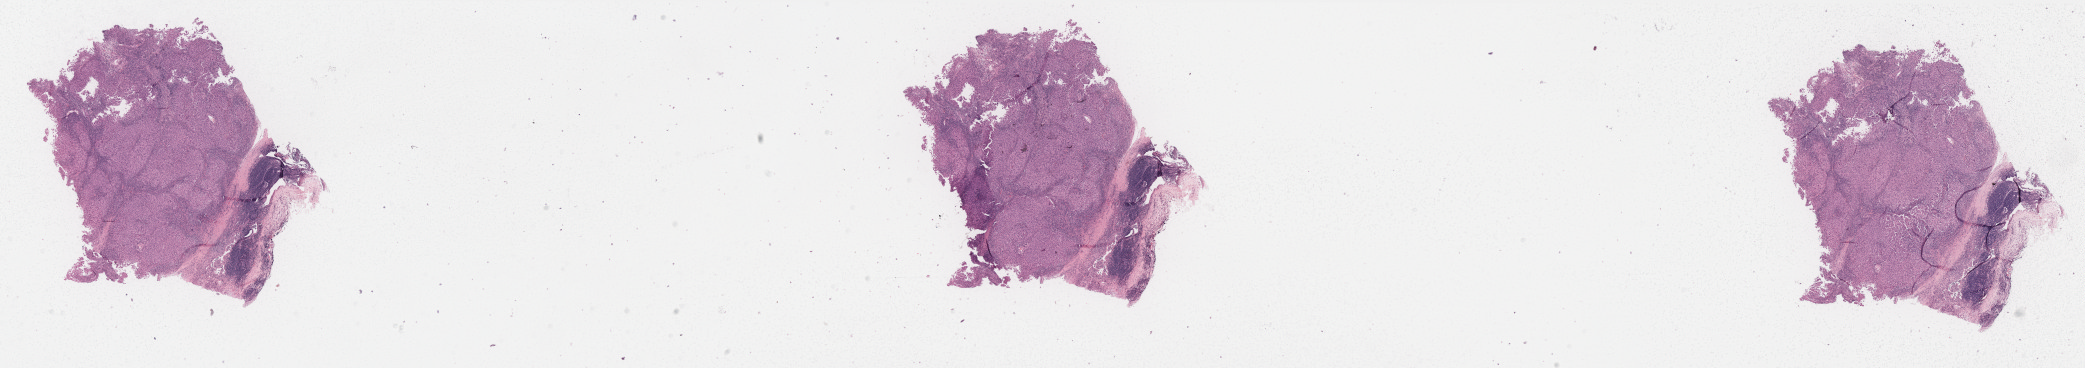
Digitized Hematoxylin and eosin (H&E) stained tissue section (whole slide) — low-resolution overview of the scanned area, about 33.4 x 5.9 mm (slide scanned at 40x). FFPE section. Primary tumour sample from the skin. Male, age 39 years at initial diagnosis.
• histologic diagnosis: Malignant melanoma, NOS